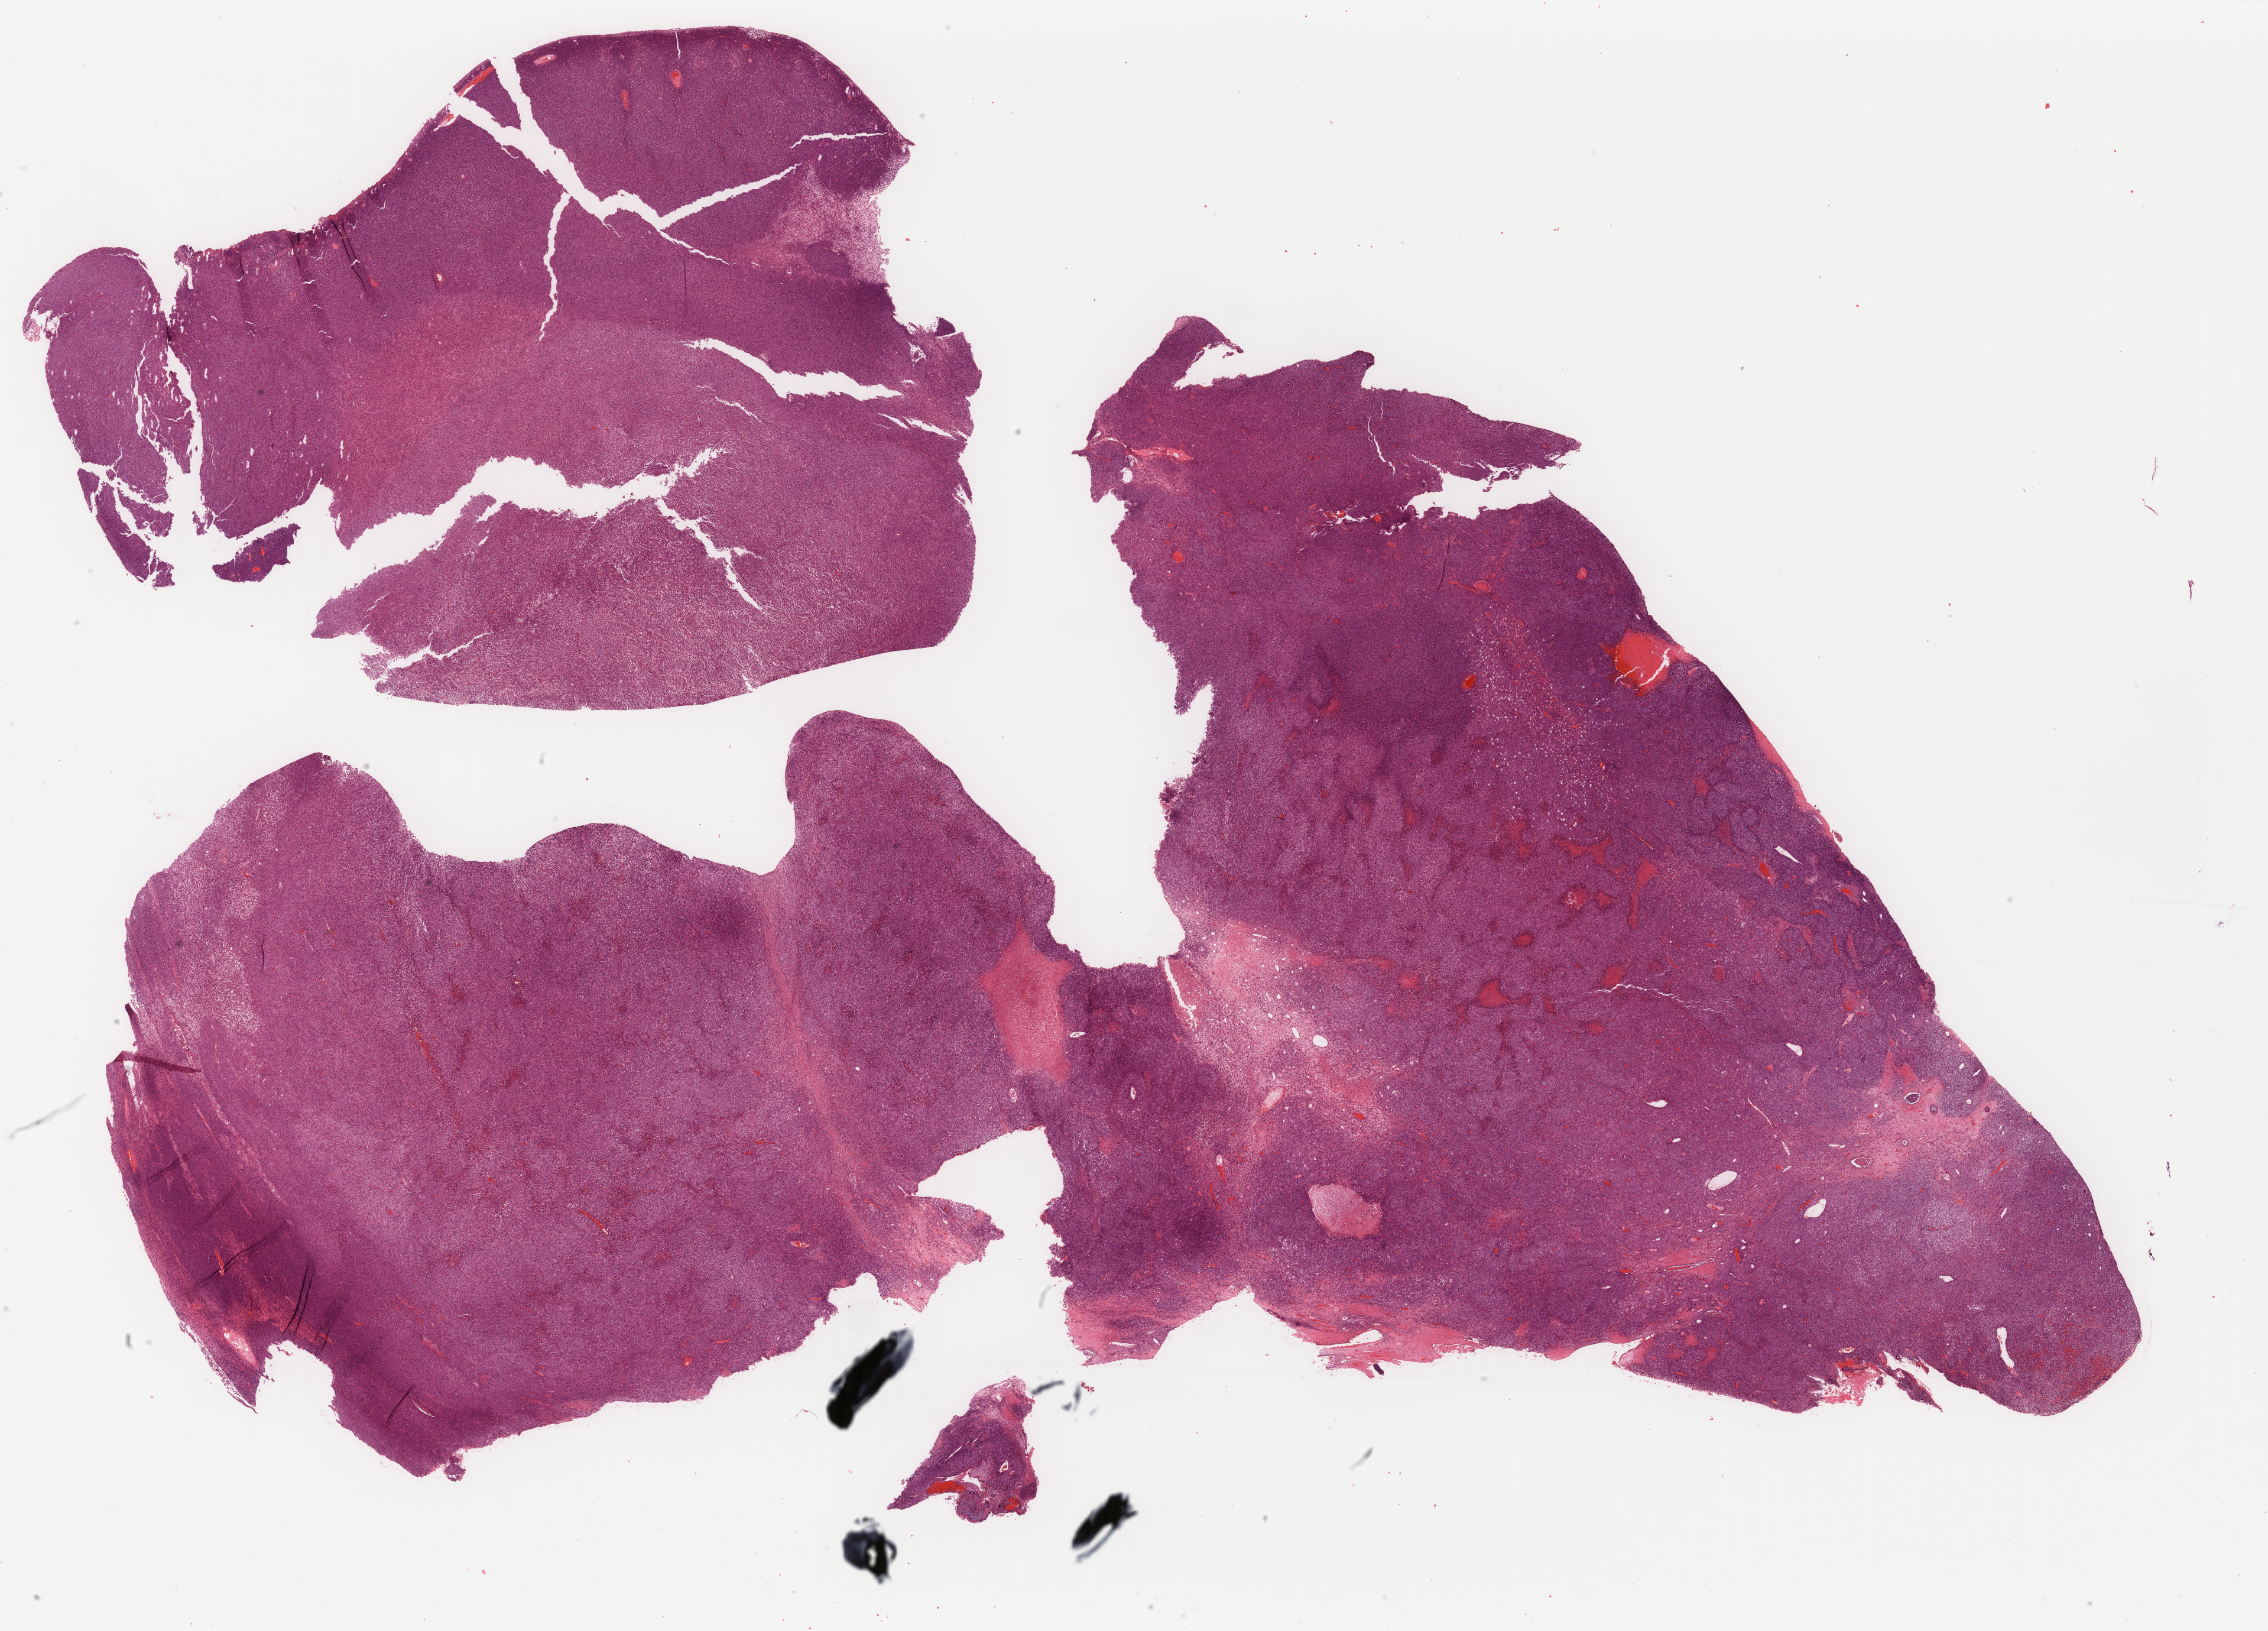
Hematoxylin and eosin (H&E) stained whole-slide image — whole scanned area (about 30.5 x 21.9 mm, acquisition: 40x scan) shown as a low-resolution overview, formalin-fixed paraffin-embedded (FFPE) diagnostic section, primary tumour sample from the uterus. Patient: female, age at initial diagnosis 72 years.
Pathologic diagnosis: Mullerian mixed tumor.